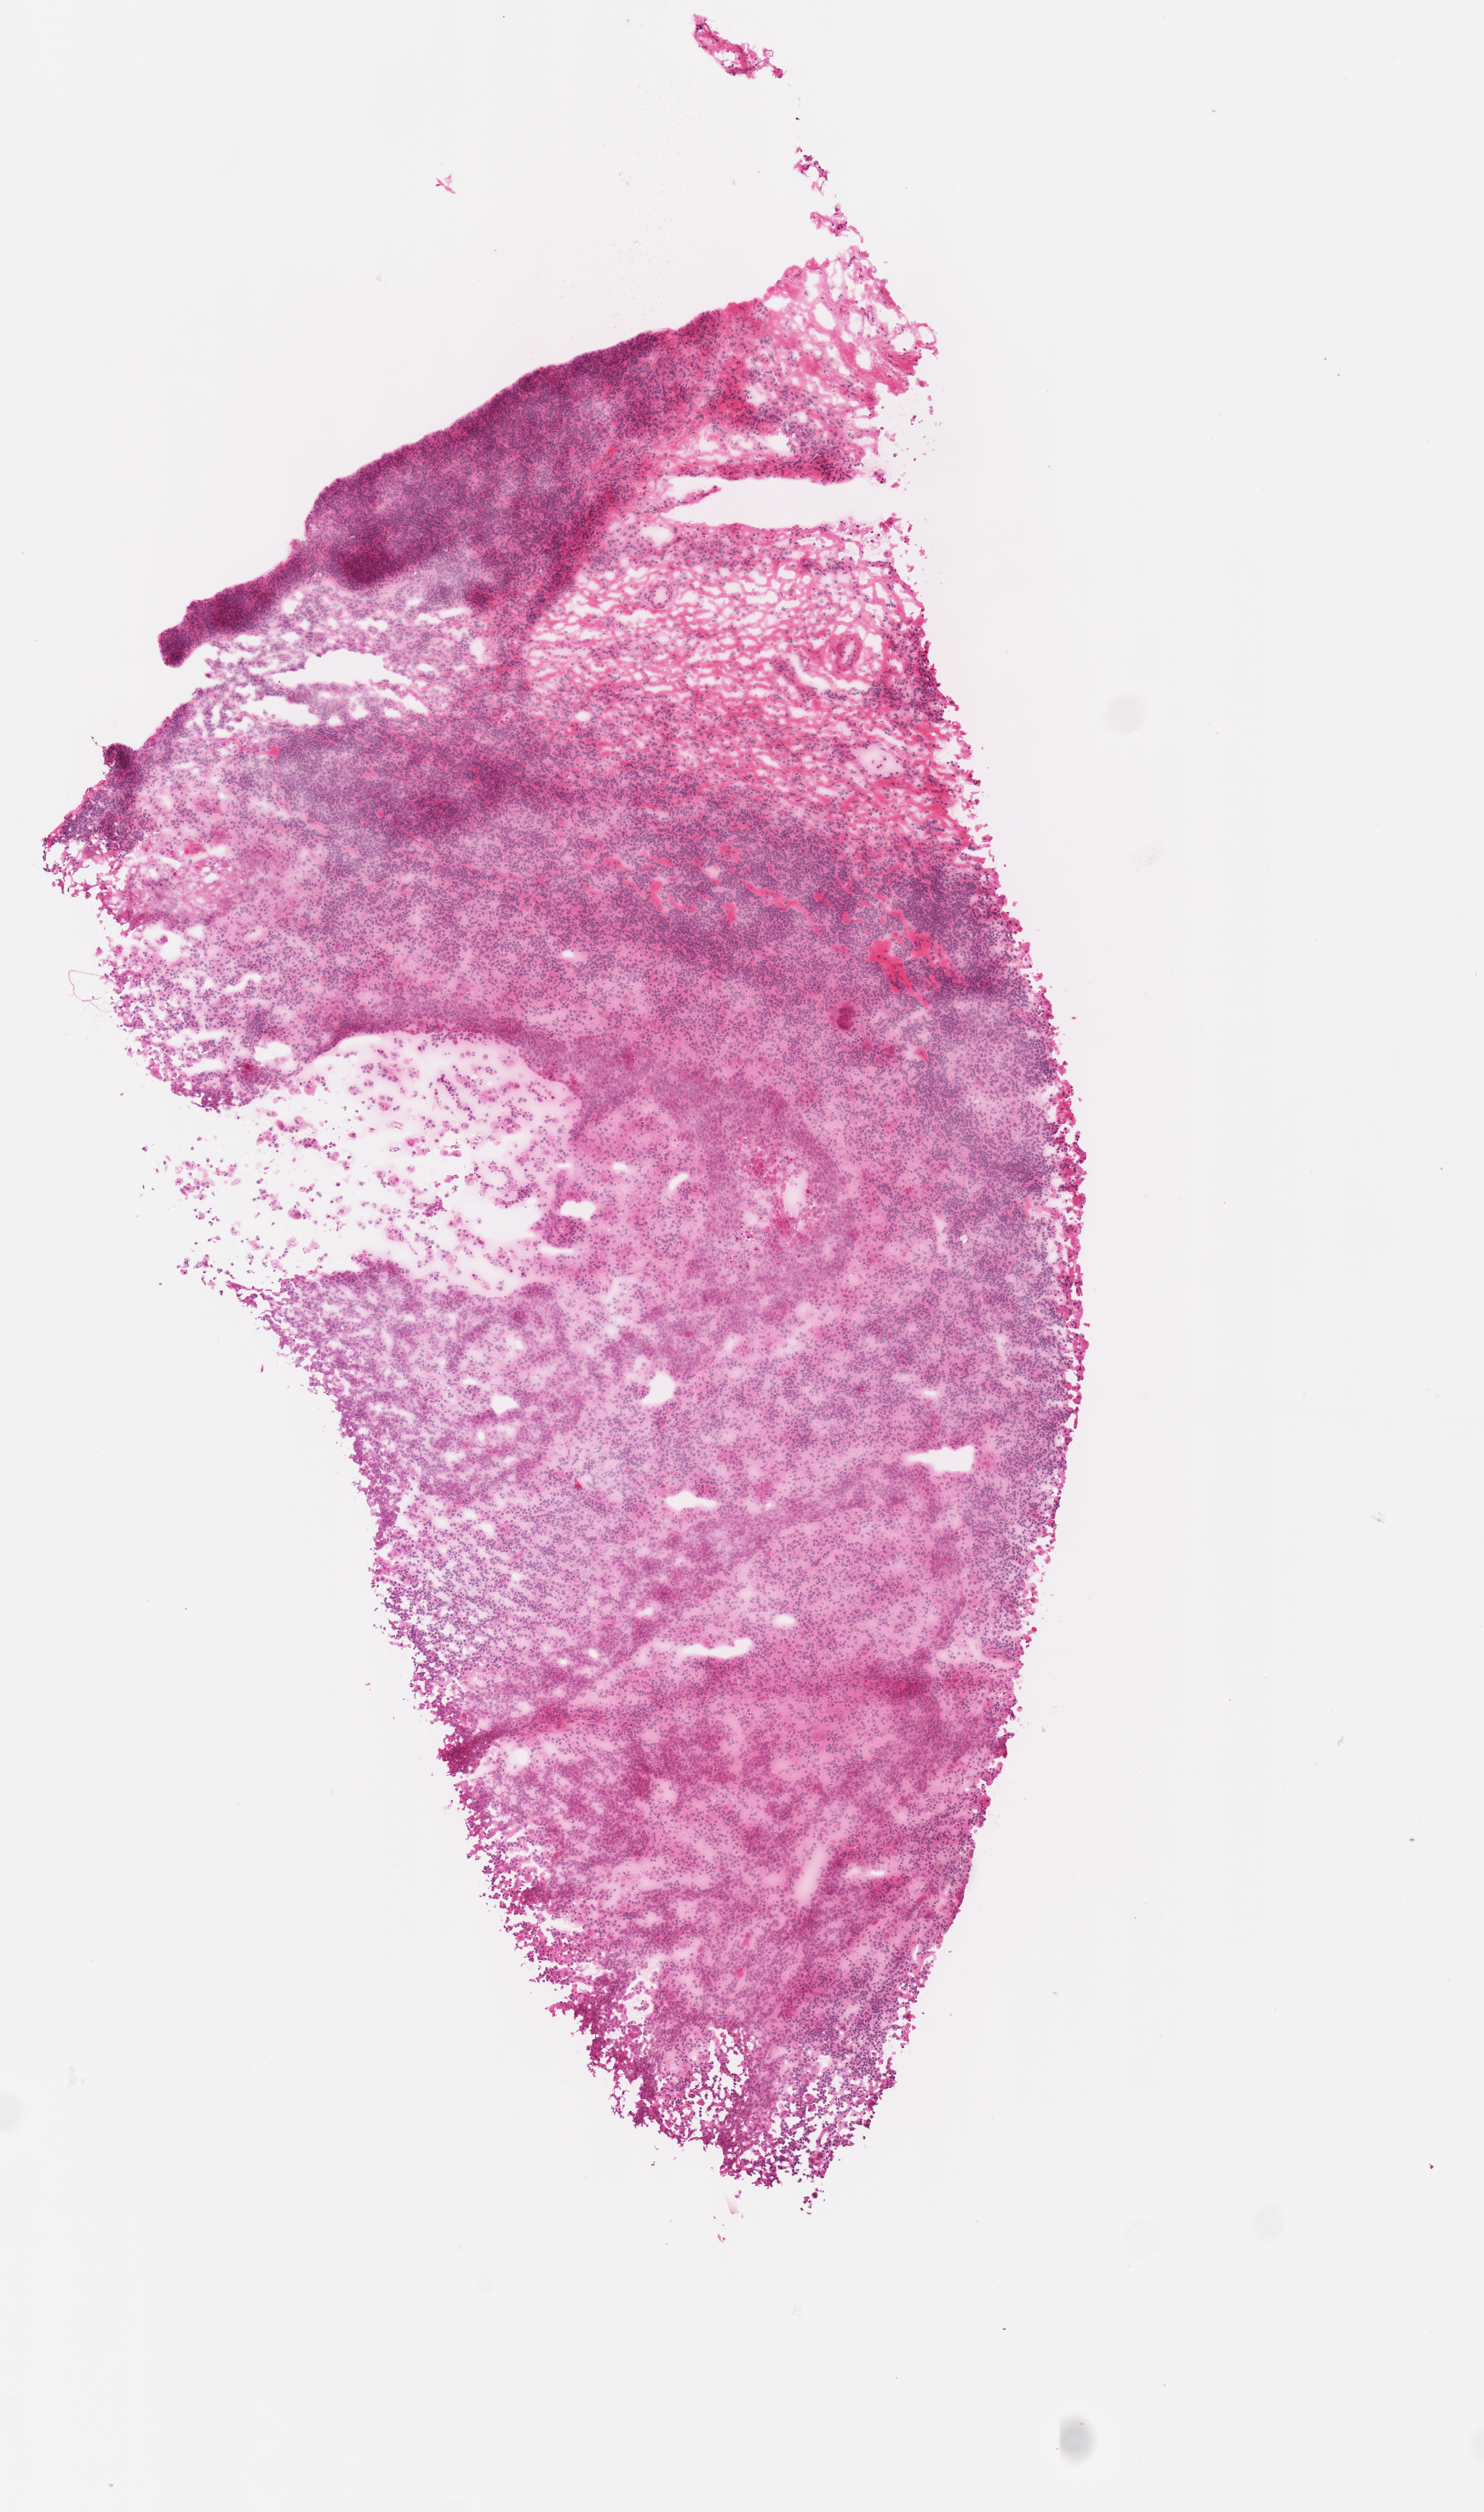
Whole-slide histology image, H&E, a low-resolution overview of the entire scanned area, about 3.4 x 5.8 mm, frozen section from the top of the tissue portion, primary tumour sample from the head and neck. Patient: male, age at initial diagnosis 56 years. Pathologist review of this section (percent, as recorded): tumour cells 70%, tumour nuclei 60%, normal cells 0%, stromal cells 27%, necrosis 3%.
• AJCC pathologic stage: III (7th edition)
• laterality: right
• diagnosis: Squamous cell carcinoma, NOS (base of tongue, NOS)